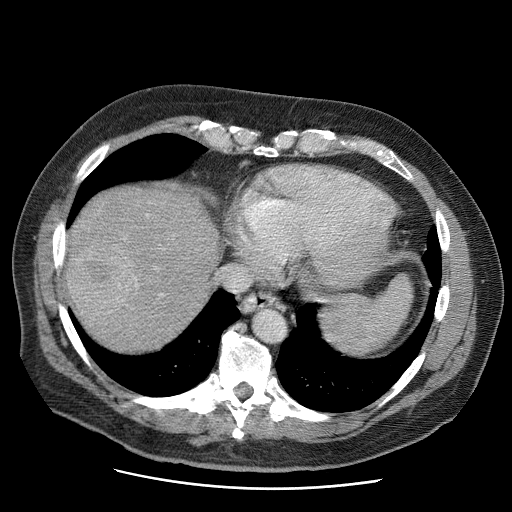
Contrast-enhanced abdominal CT (liver protocol), one axial slice; position 55 of 81 along the scan axis; soft-tissue window (W 400 / L 40 HU); 512 × 512 image matrix, field of view 380 × 380 mm. Case-level facts recorded for this patient, not image findings: diagnosis: hepatocellular carcinoma (patient treated with transarterial chemoembolisation; whether this scan precedes or follows treatment is not stated here); TNM stage (as recorded): Stage-IIIA; Child-Pugh class: A; tumour differentiation: moderately differentiated.
Outlined on this slice (semi-automatic segmentation, software-assisted and operator-edited):
- liver parenchyma outside the tumour (the mass and vessels are separate outlines, so this box may not span the whole liver): bounding box [x1, y1, x2, y2] px = [64, 186, 218, 351]
- mass: [64, 240, 141, 318]